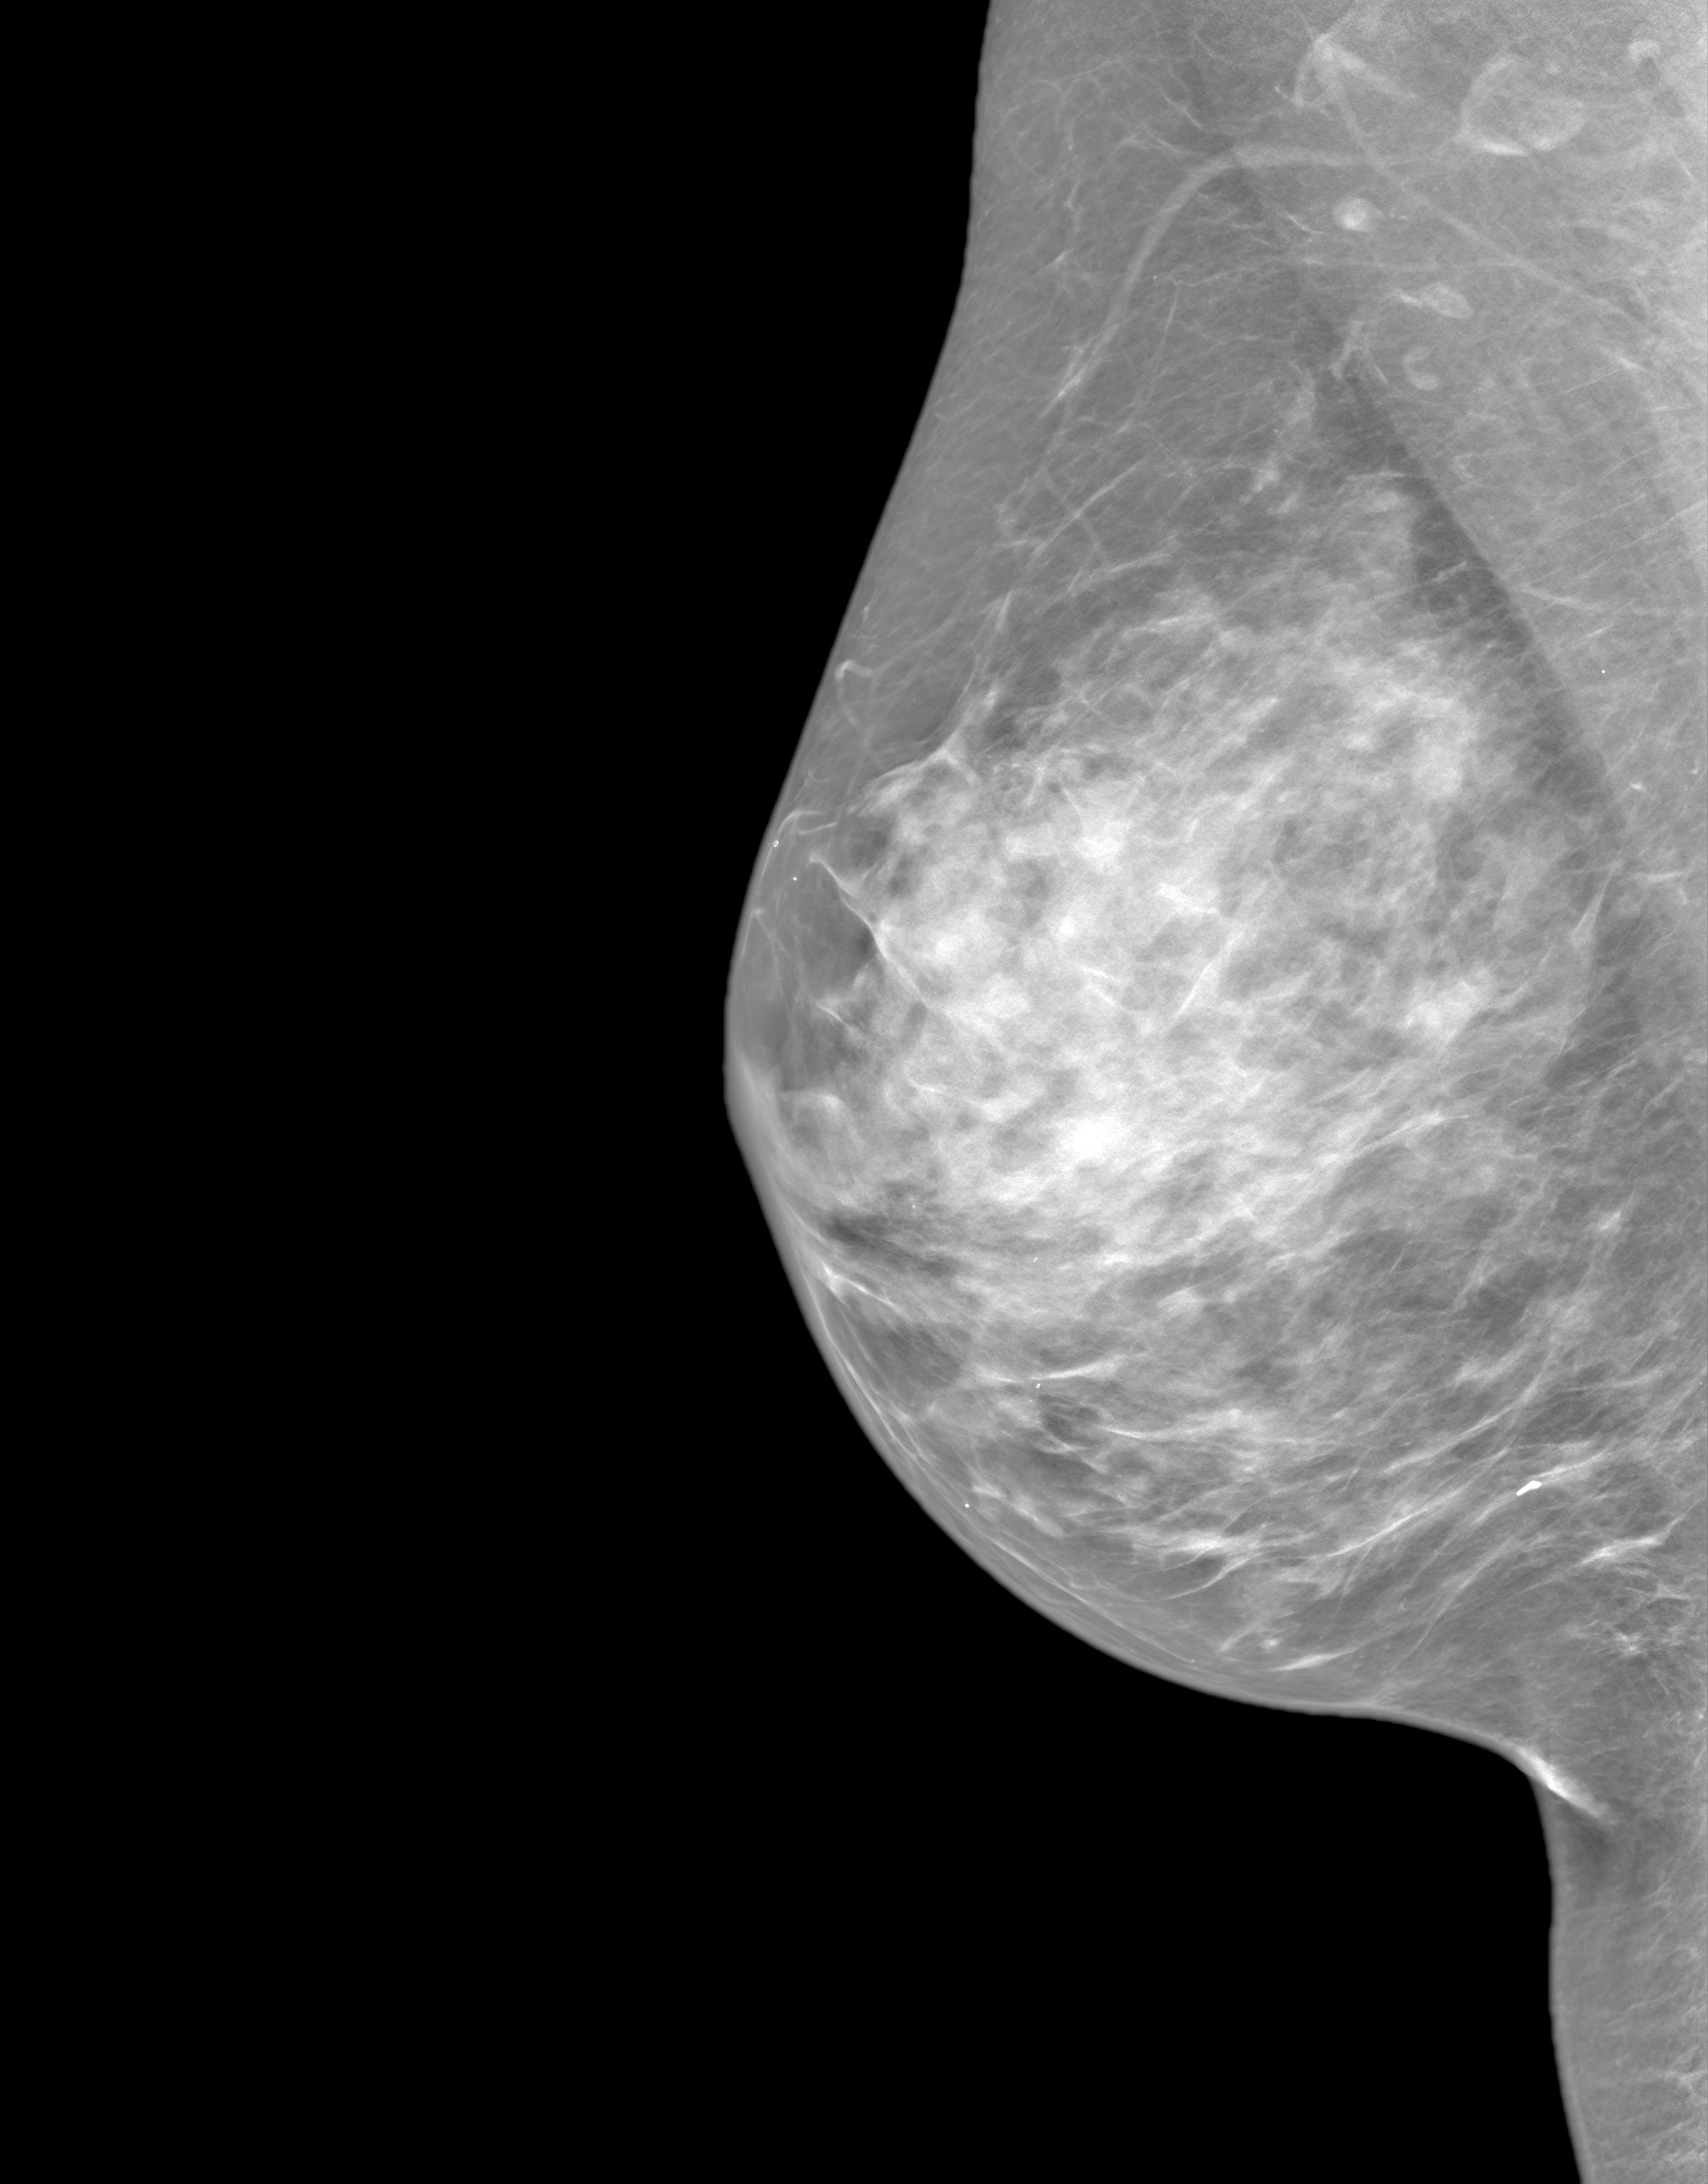
Synthetic 2-D view generated from a tomosynthesis acquisition (not an FFDM exposure); right breast; medio-lateral oblique projection; annual screening mammography examination; system: SenoIris_1SP1.1(421). Patient: female, 64 years.
Breast density at the screening exam (both breasts): extremely dense (BI-RADS density category d). Final BI-RADS assessment for this screening round (tomosynthesis exam, both breasts): category 2. Recall: no recall after this screen.